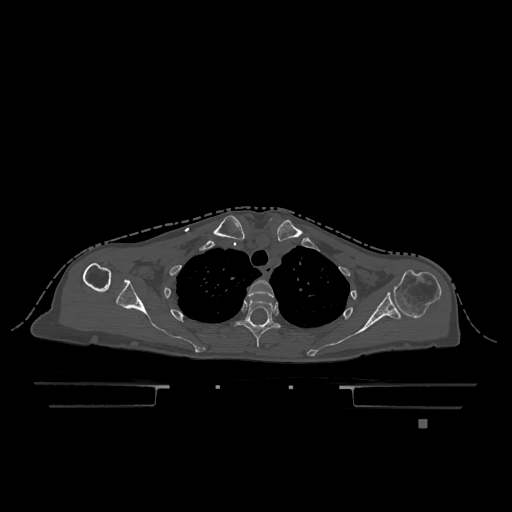
CT including the spine, one axial slice; slice 929 of 1317 in the series (ordered by position); bone window (W 1800 / L 400 HU); 512 × 512 image matrix, field of view 500 × 500 mm. Female patient, age 74 years. From the clinical record (not read from this slice): primary cancer: lung.
Outlined on this slice (semi-automatically segmented with operator editing):
- T2 vertebra: bounding box [x1, y1, x2, y2] px = [247, 280, 274, 297]
- T3 vertebra: [234, 299, 280, 347]